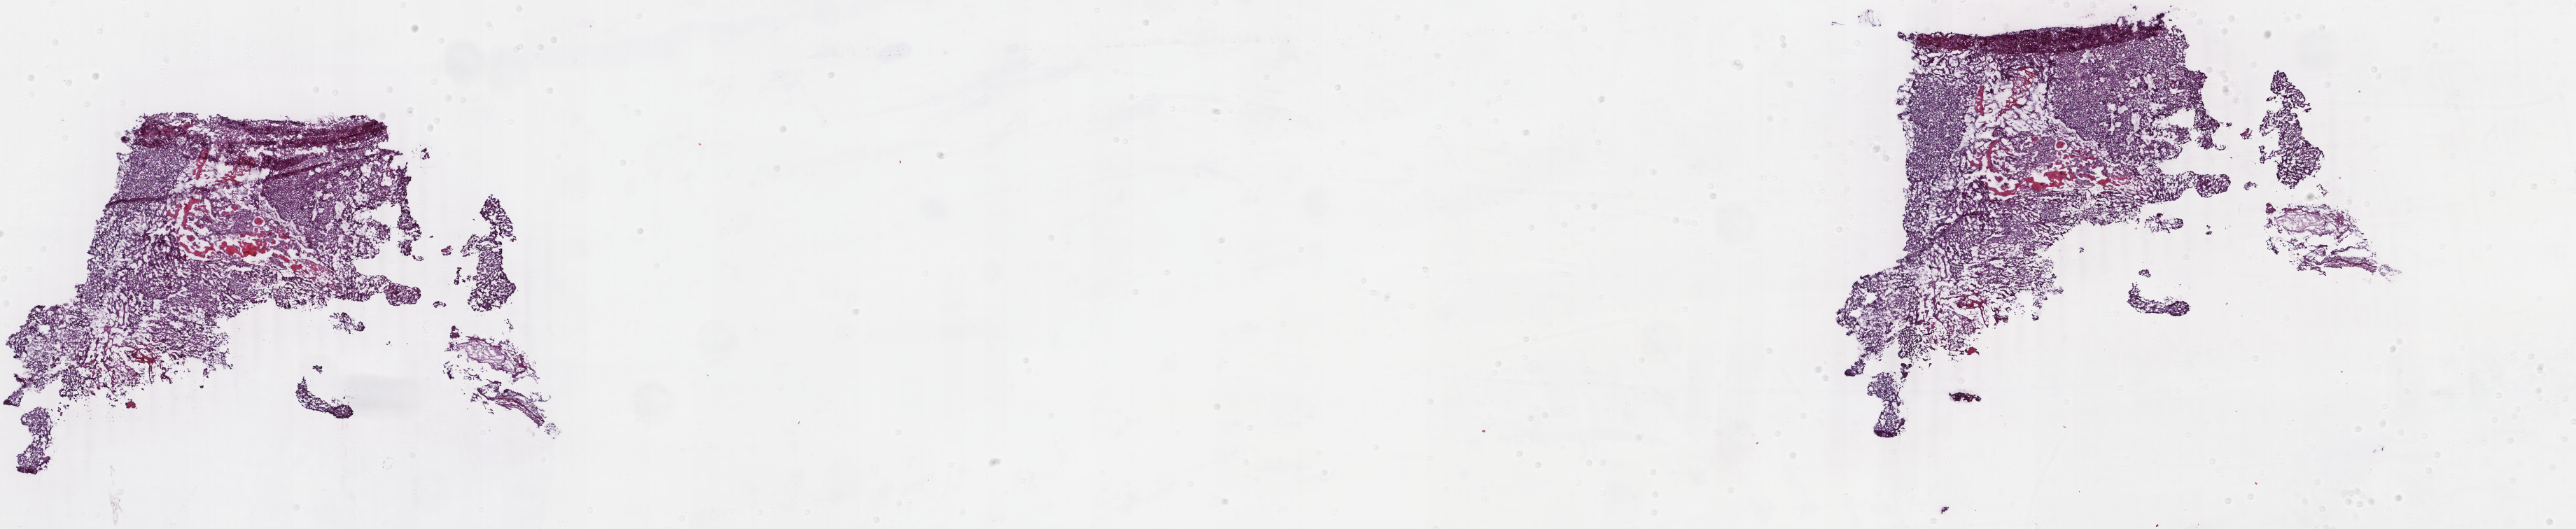
H&E-stained whole-slide image, whole scanned area (about 29.3 x 6.0 mm) shown as a low-resolution overview, frozen section from the top of the tissue portion, primary tumour sample from the uterus. Female patient; age at initial diagnosis 71 years.
Histologic diagnosis: Endometrioid adenocarcinoma, NOS (endometrium).